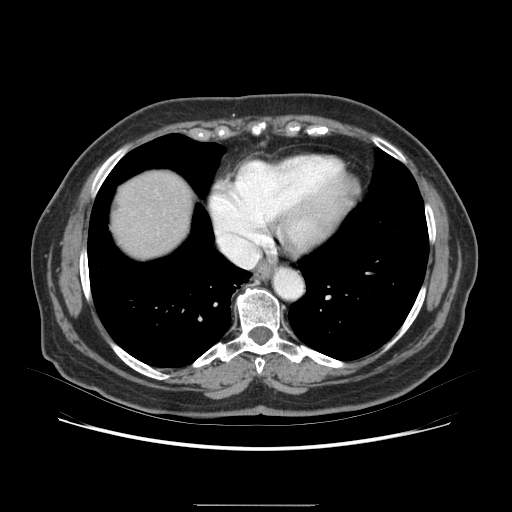
Contrast-enhanced abdominal CT (liver protocol), one axial slice. Position 75 of 79 along the scan axis. 120 kVp. Soft-tissue window (W 400 / L 40 HU). 512 × 512 image matrix. Case-level facts recorded for this patient, not image findings: diagnosis: hepatocellular carcinoma (patient treated with transarterial chemoembolisation; whether this scan precedes or follows treatment is not stated here); TNM stage (as recorded): Stage-I; Child-Pugh class: A.
Outlined on this slice (semi-automatic segmentation, software-assisted and operator-edited):
- liver parenchyma outside the tumour (the mass and vessels are separate outlines, so this box may not span the whole liver): bounding box (x1, y1, x2, y2) in pixels: (156, 186, 164, 190)